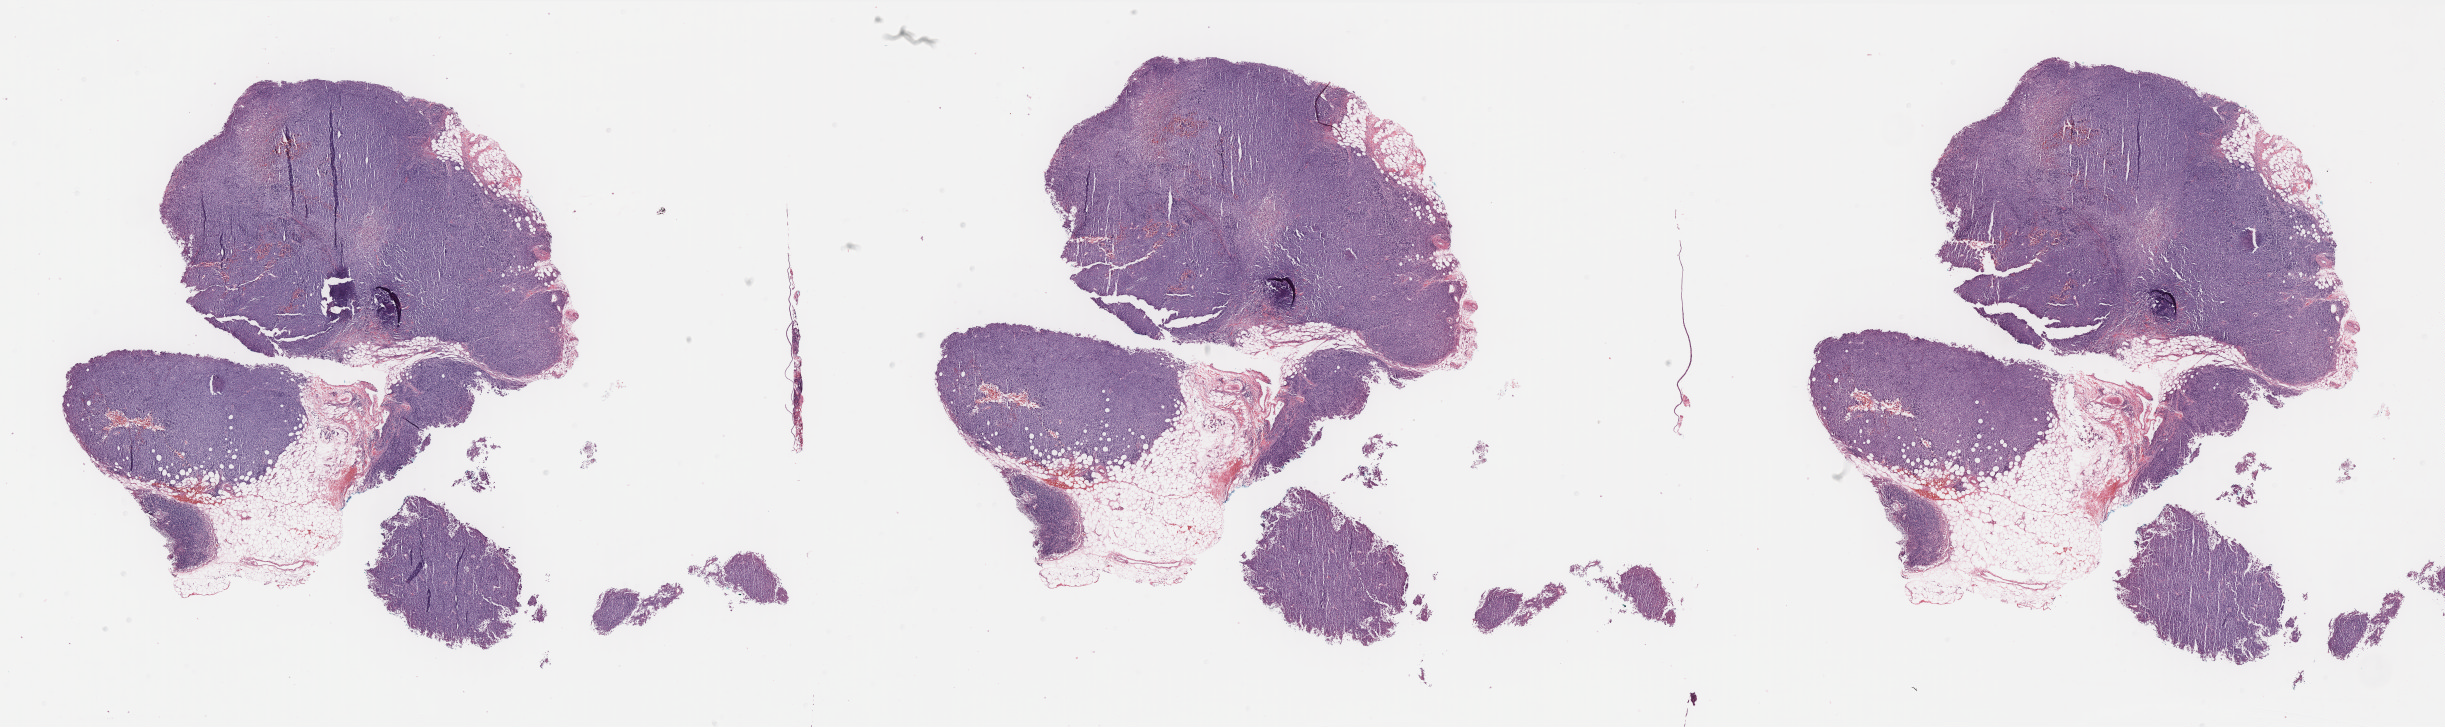
Digitized Hematoxylin and eosin (H&E) stained tissue section (whole slide) — shown as a low-resolution overview of the whole scanned area (about 39.2 x 11.7 mm), FFPE section, skin, primary tumour sample. Male, age 52 years at initial diagnosis.
Diagnosis: Malignant melanoma, NOS.